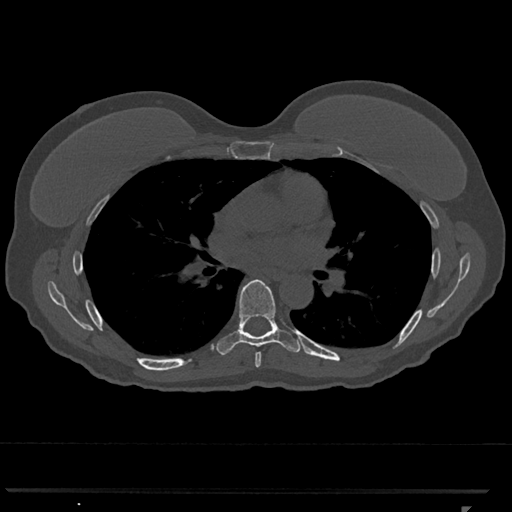
CT including the spine, one axial slice. Position 720 of 793 along the scan axis. Reconstruction kernel Br40s/3. 120 kVp. Bone window (W 1800 / L 400 HU). 0.5 mm slice thickness. 512 × 512 image matrix, field of view 380 × 380 mm. Female patient, age 62 years. From the clinical record (not read from this slice): primary cancer: renal.
Annotated regions visible in this slice (semi-automatically segmented with operator editing):
- T6 vertebra: bounding box [x1, y1, x2, y2] px = [255, 352, 262, 368]
- T7 vertebra: [217, 279, 302, 355]